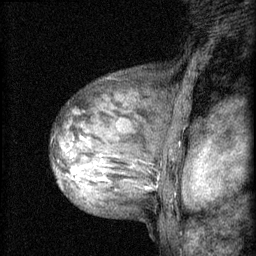
Breast MRI (dynamic contrast-enhanced), one sagittal slice; position 44 of 60 along the scan axis; 3 images stored at this slice position (order not interpretable as contrast timing); 1.5 T; TE 4.2 ms, TR 8.2 ms; 2 mm slice thickness; 256 × 256 image matrix, field of view 180 × 180 mm. Female patient, age 48 years.
Annotated regions visible in this slice (semi-automatic segmentation, software-assisted and operator-edited):
- analysis volume of interest (the breast-tissue region the enhancement analysis was run in; not a lesion): bounding box (x1, y1, x2, y2) in pixels: (56, 138, 133, 191)
- tumour enhancement mask (voxels above the 70 % enhancement threshold inside the analysis volume of interest): (72, 138, 101, 181)